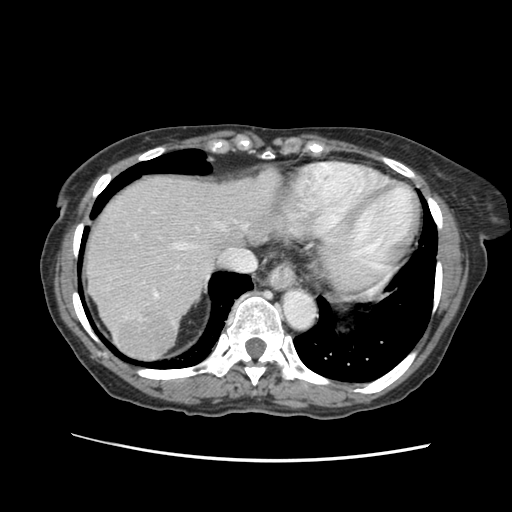
Contrast-enhanced abdominal CT (liver protocol), one axial slice; slice 50 of 63 in the series (ordered by position); reconstruction kernel STANDARD; 120 kVp; soft-tissue window (W 400 / L 40 HU); 512 × 512 image matrix, field of view 340 × 340 mm. Case-level facts recorded for this patient, not image findings: diagnosis: hepatocellular carcinoma (patient treated with transarterial chemoembolisation; whether this scan precedes or follows treatment is not stated here); TNM stage (as recorded): Stage-I; Child-Pugh class: B; tumour differentiation: well differentiated.
Annotated regions visible in this slice (semi-automatic segmentation, software-assisted and operator-edited):
- liver parenchyma outside the tumour (the mass and vessels are separate outlines, so this box may not span the whole liver): bounding box <86,168,281,356> (left, top, right, bottom; pixels)
- mass: <105,292,178,356>
- liver vessels: <153,210,269,297>